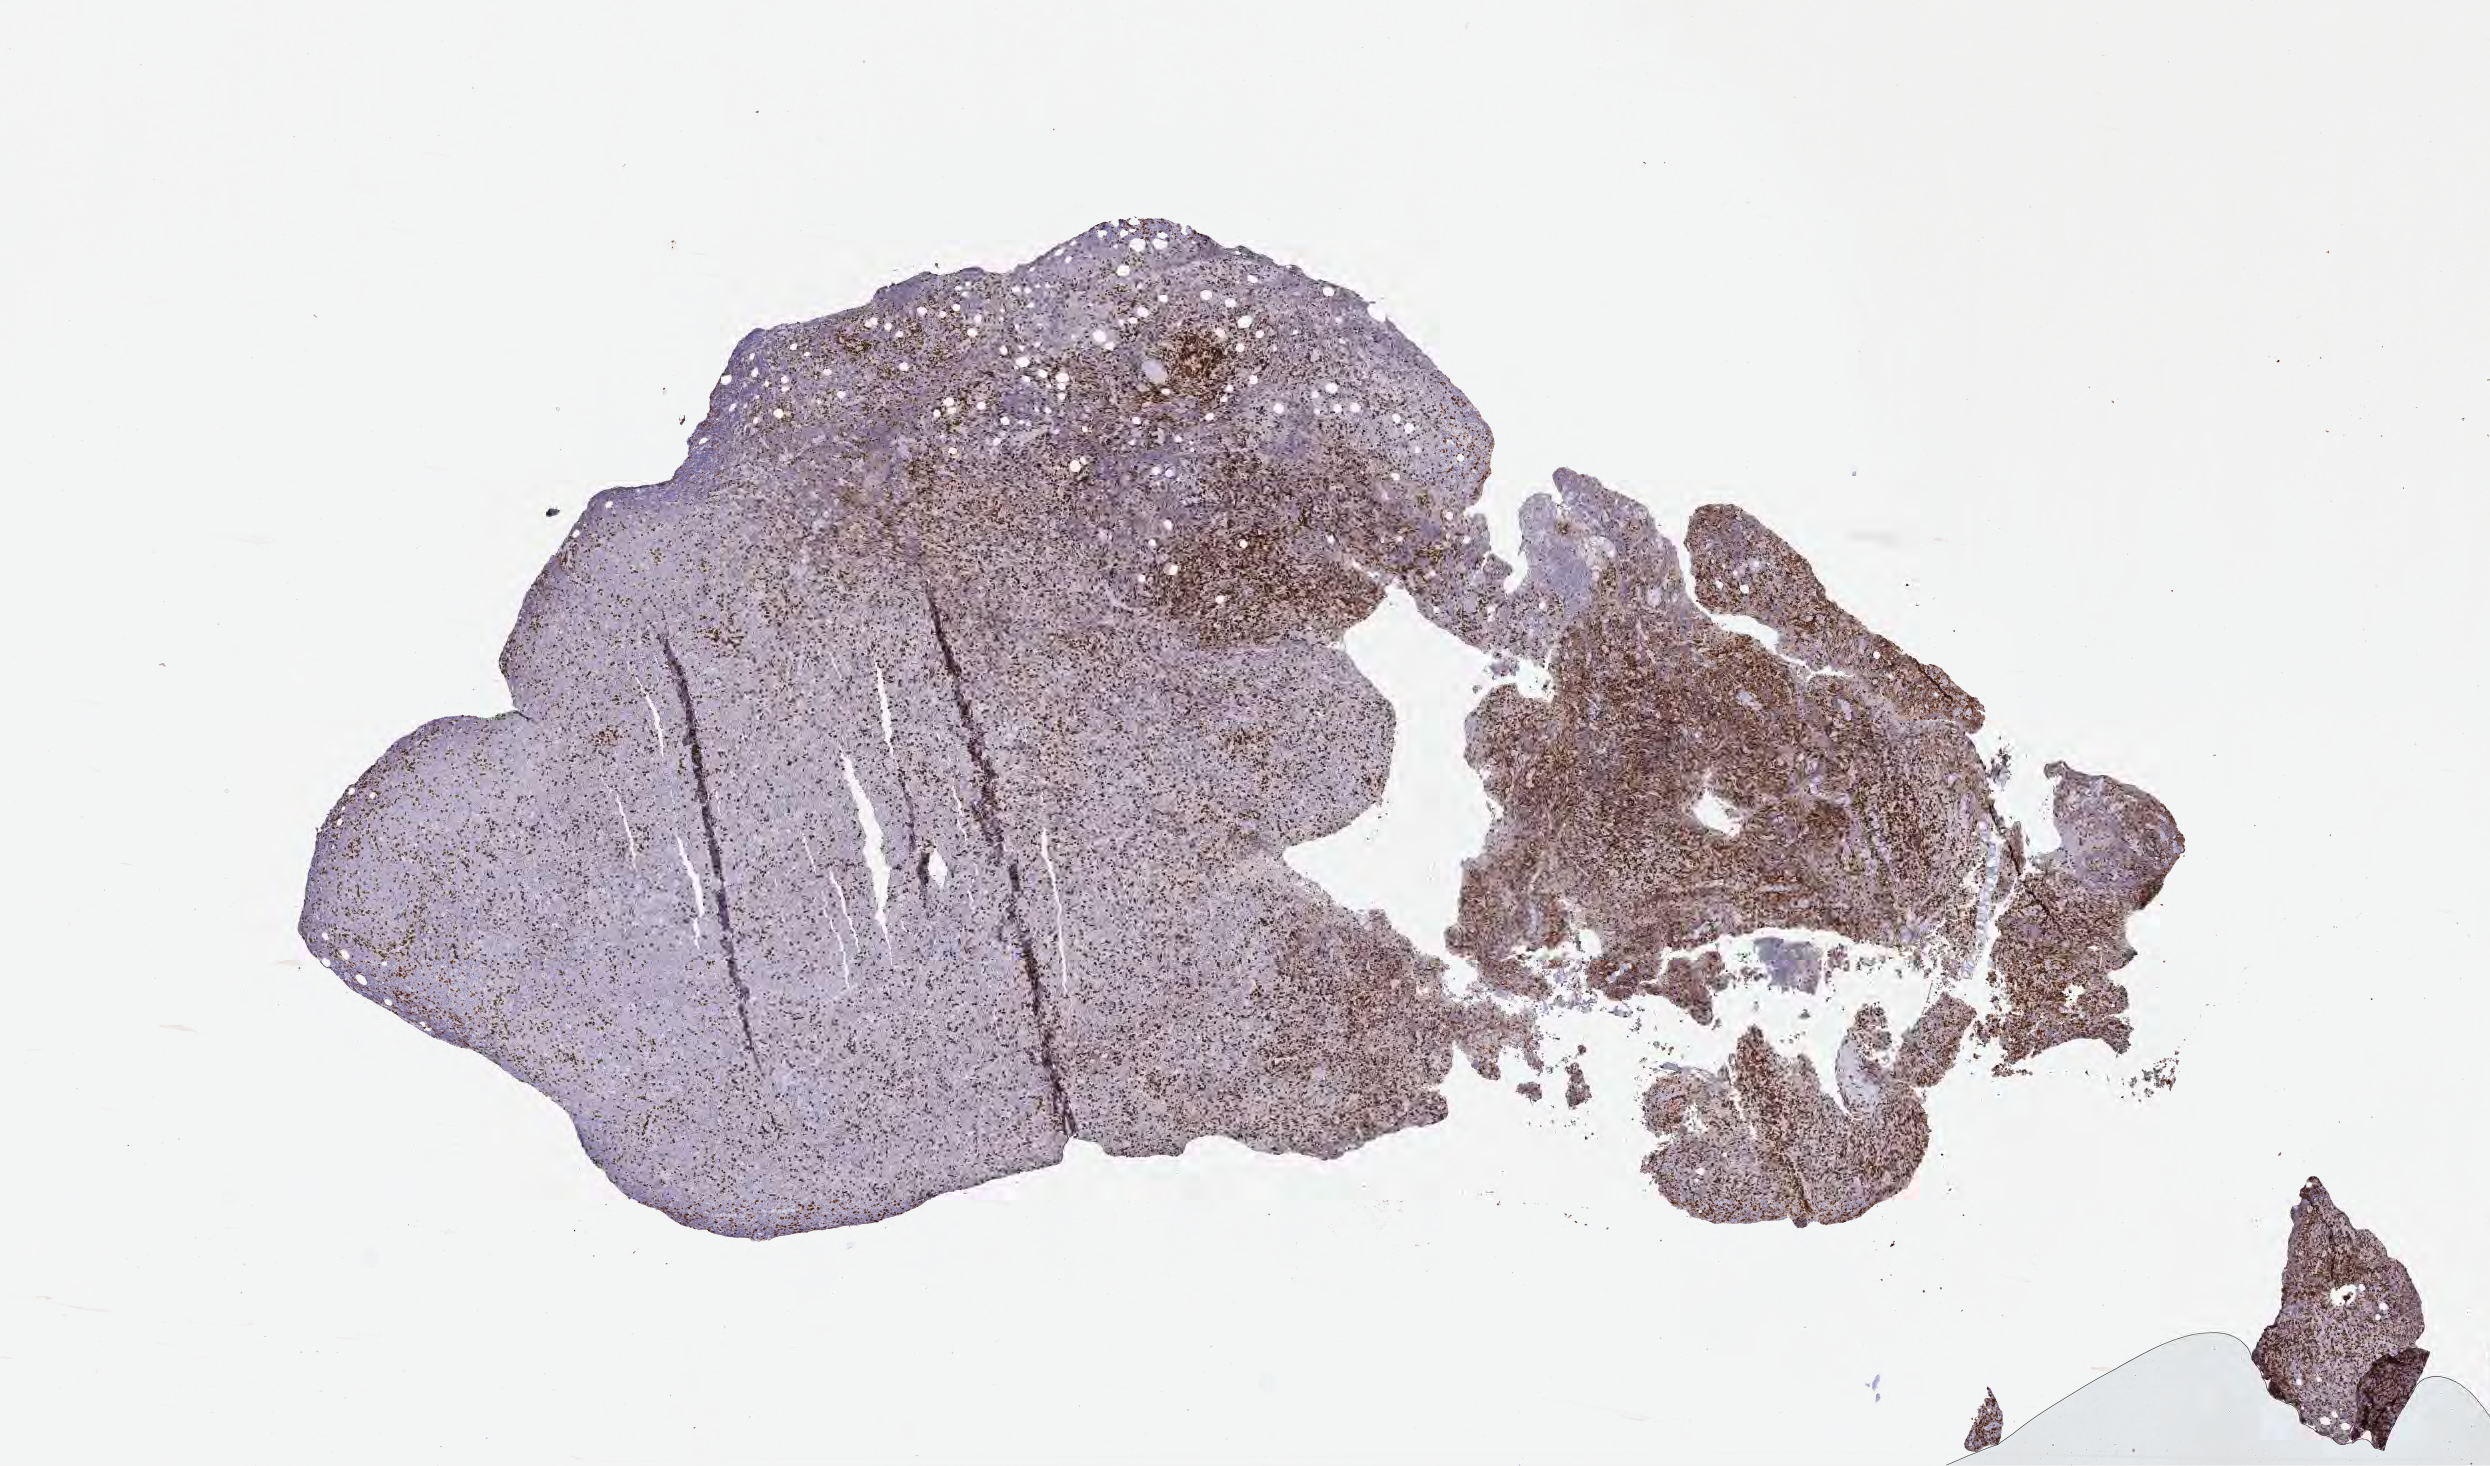
Immunohistochemistry (IHC) whole-slide image stained for CD3 — whole scanned area (about 10.1 x 5.9 mm) shown as a low-resolution overview. Specimen: tumor tissue. Patient: female, aged 40.
* diagnosis: Burkitt lymphoma, NOS